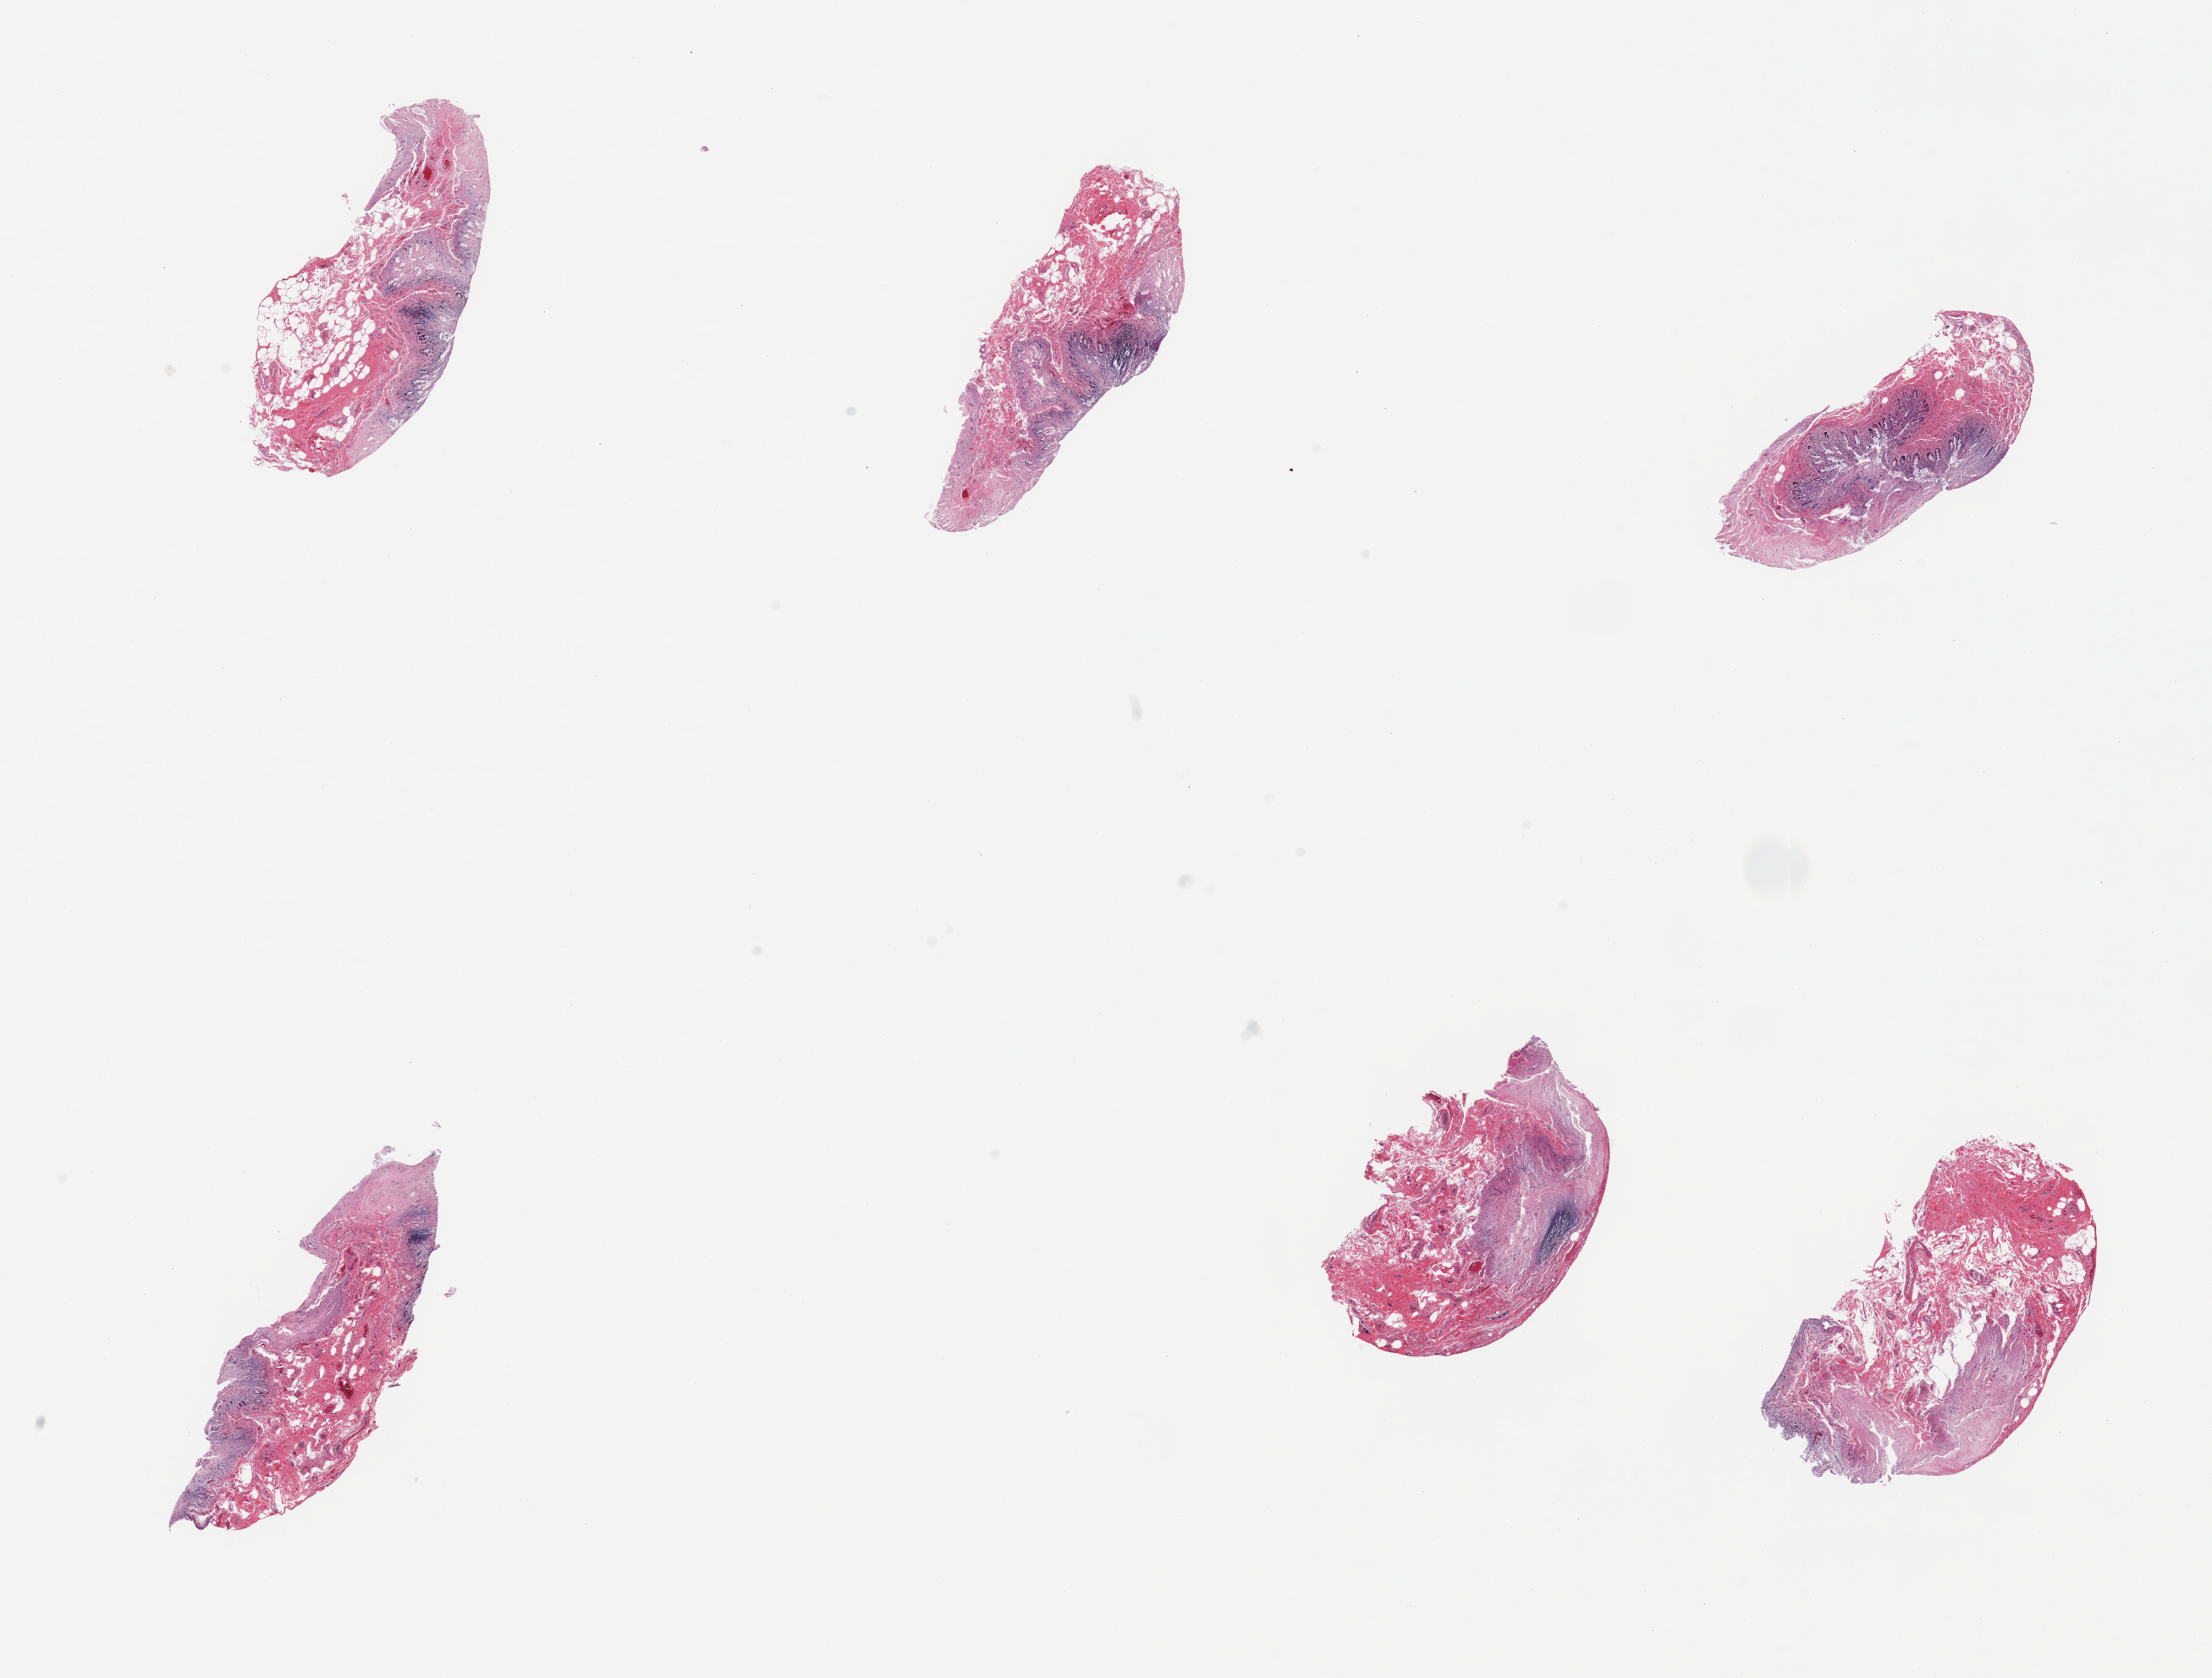
Whole-slide image, H&E stain — low-resolution overview of the scanned area, about 20.7 x 15.7 mm (from a 20x scan). PAXgene-fixed paraffin-embedded (PFPE) section. Sampled site (target tissue): ileum. Tissue donor sample. Donor: male.
Reviewer comment on this tissue sample: 6 pieces; autolyzed mucosa with no significant residual lymphoid aggregates.